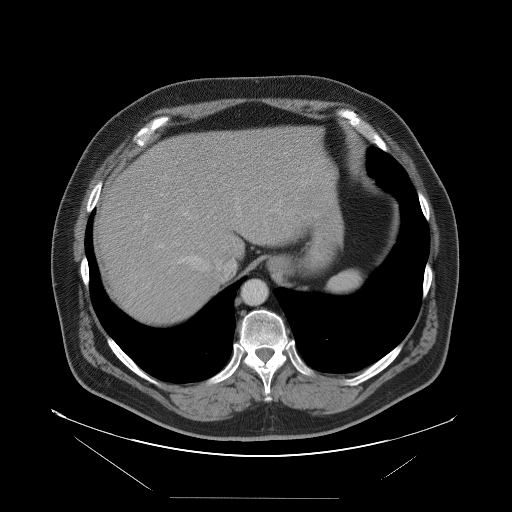
Contrast-enhanced abdominal CT, one axial slice. Position 81 of 114 along the scan axis. Intravenous contrast given. Soft-tissue window (W 400 / L 40 HU). 5 mm slice thickness. 512 × 512 image matrix. Male patient, age 61 years. Case-level facts recorded for this patient, not image findings: diagnosis: colorectal cancer liver metastases, imaged before liver resection; multiple liver metastases: no; largest metastasis: 6.5 cm.
Annotated regions visible in this slice (outlined manually by an expert reader):
- hepatic veins: box from (x=170, y=207) to (x=282, y=278) px
- liver: (x=97, y=127)–(x=321, y=326)
- planned liver remnant (the part of the liver to remain after resection): (x=148, y=127)–(x=322, y=265)
- portal vein (with intrahepatic branches): (x=144, y=214)–(x=164, y=248)